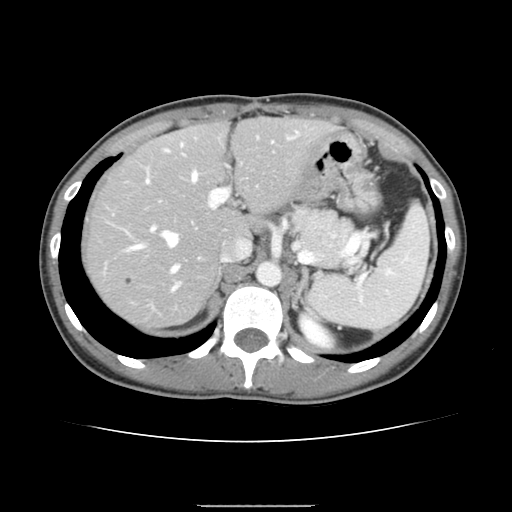
Contrast-enhanced abdominal CT, one axial slice; position 104 of 150 along the scan axis; intravenous contrast given; soft-tissue window (W 400 / L 40 HU); 512 × 512 image matrix, field of view 324 × 324 mm. Female patient, age 32 years. Case-level facts recorded for this patient, not image findings: diagnosis: colorectal cancer liver metastases, imaged before liver resection; multiple liver metastases: yes; largest metastasis: 0.7 cm; chemotherapy before resection: yes.
Annotated regions visible in this slice (manually delineated by an expert):
- hepatic veins: bounding box <131,172,197,271> (left, top, right, bottom; pixels)
- liver: <87,119,331,328>
- planned liver remnant (the part of the liver to remain after resection): <87,120,329,281>
- portal vein (with intrahepatic branches): <146,132,300,291>
- liver metastasis: <125,277,133,285>